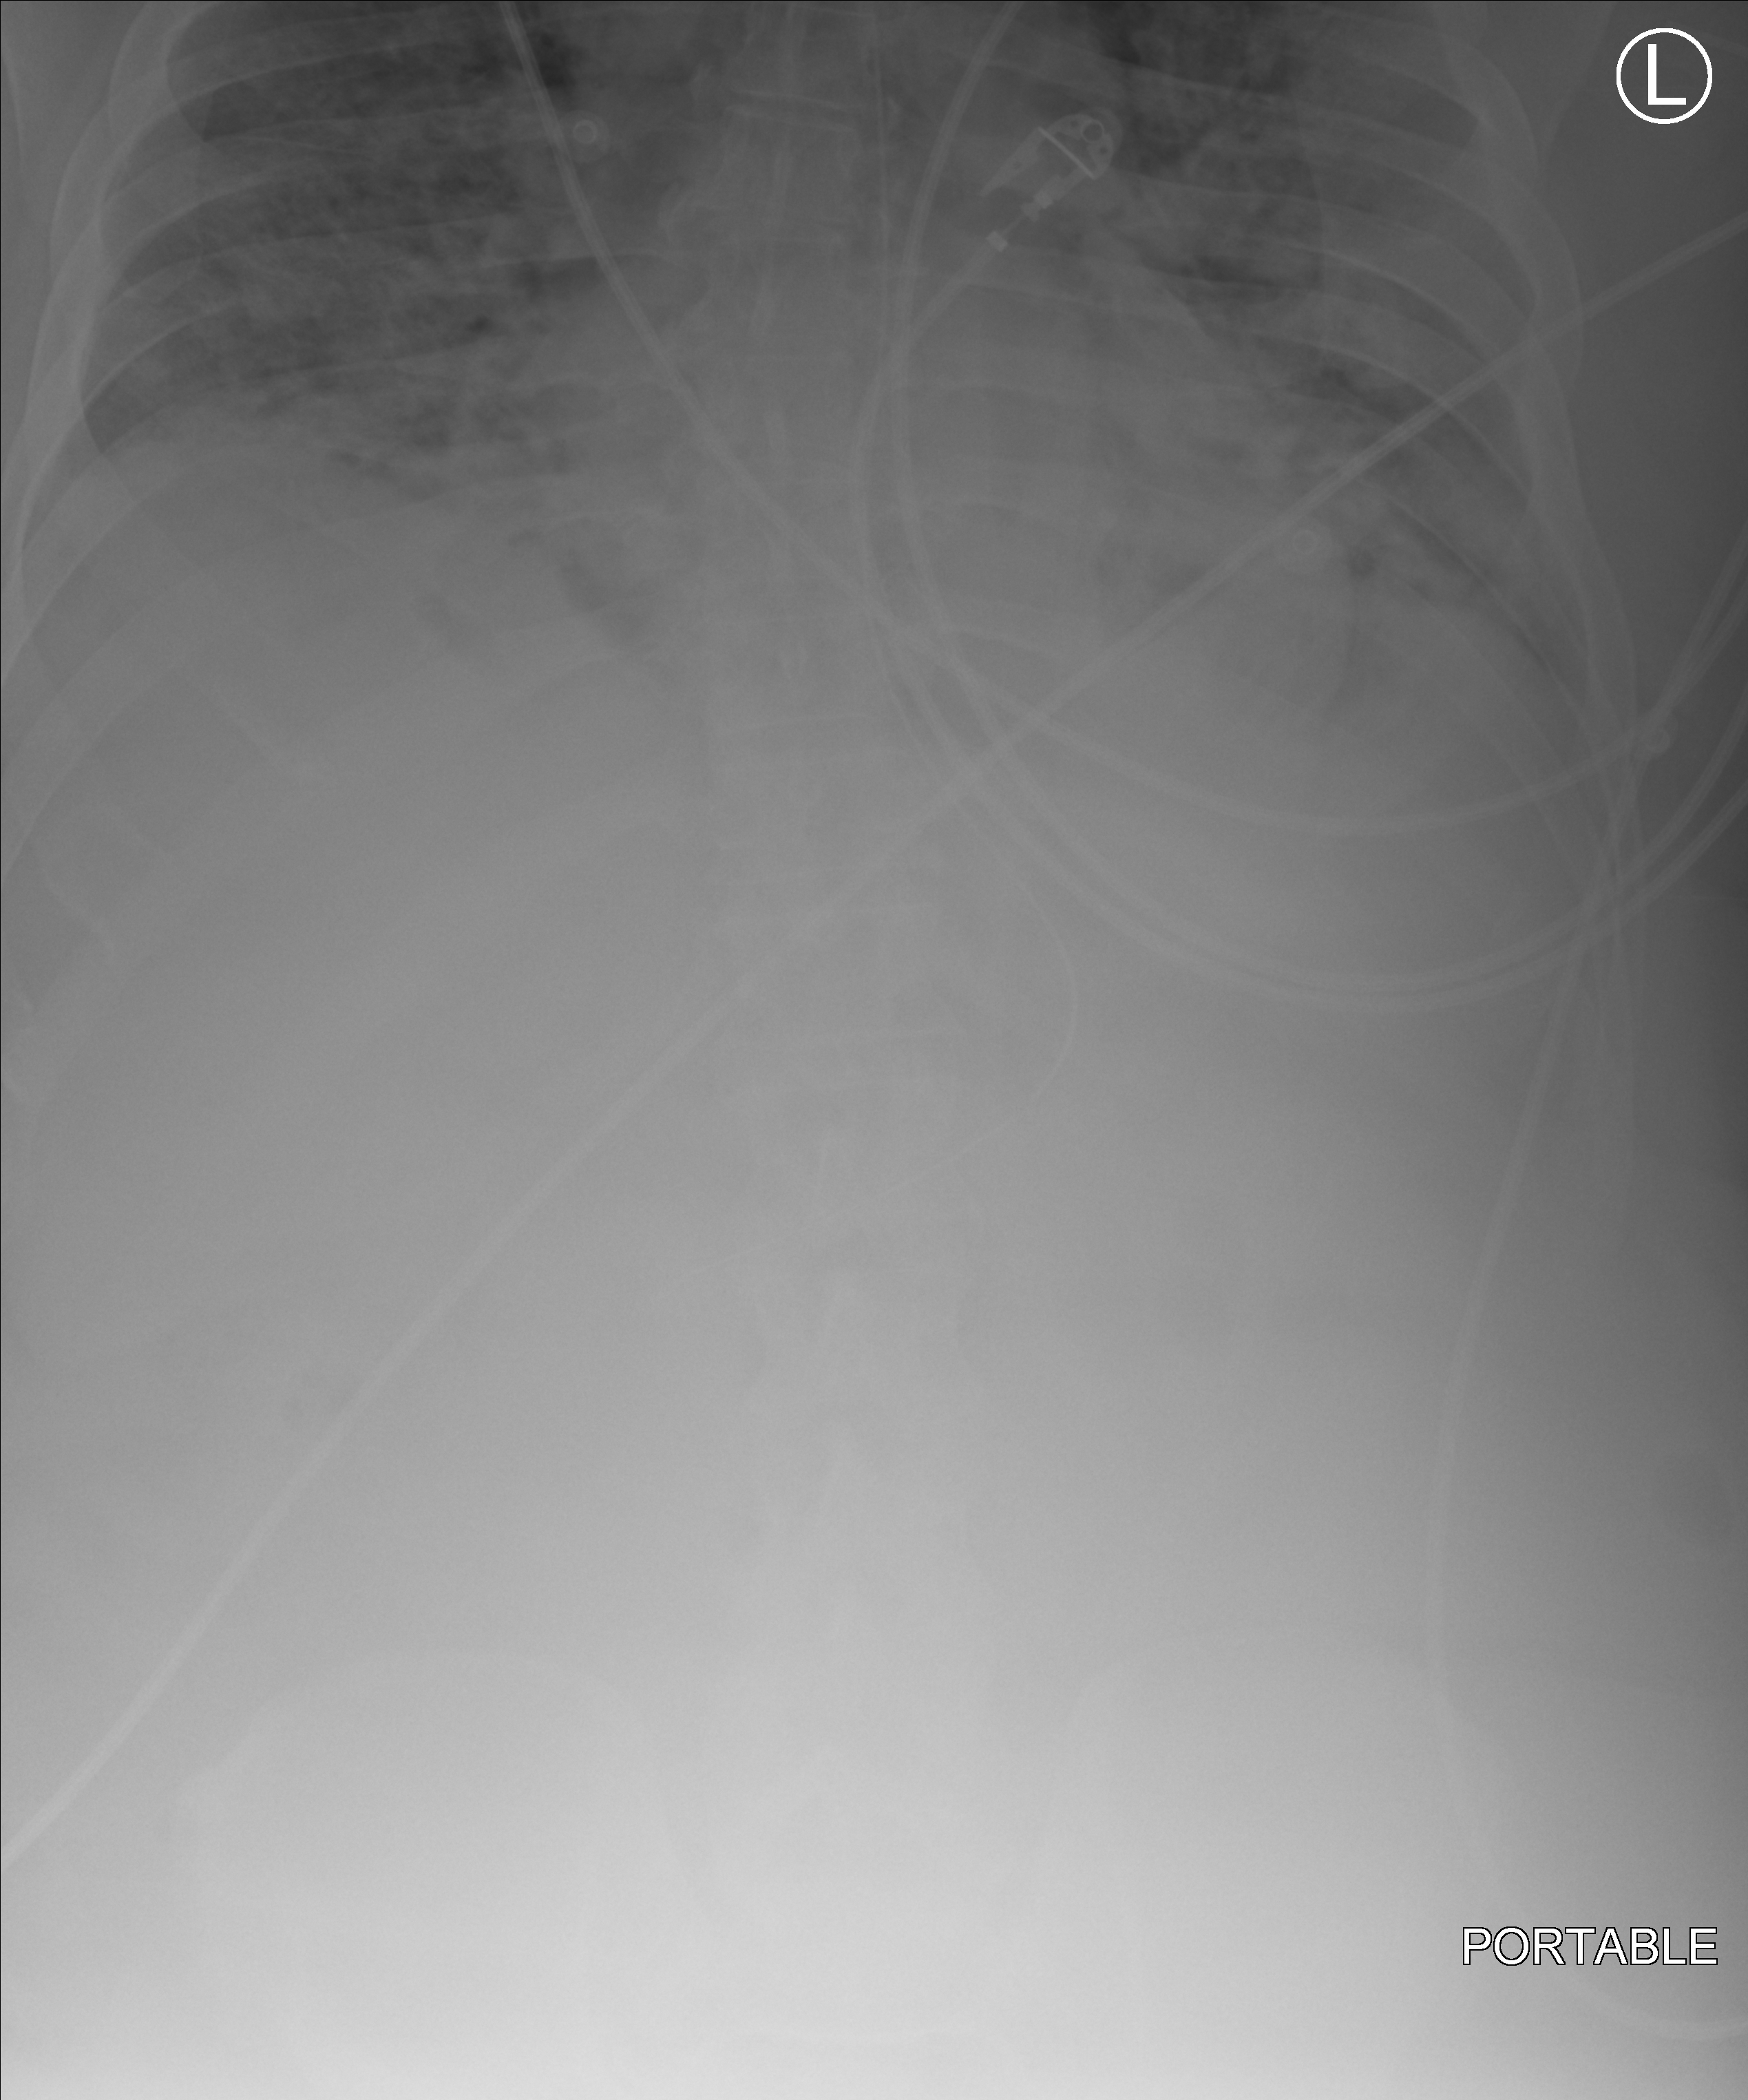
Portable chest radiograph, anteroposterior (AP) projection. Male patient hospitalised with COVID-19, age 18–59 years.
Hospital-stay facts (about this admission, not read from this image; timing relative to this image not recorded):
- admitted to intensive care during this hospital stay: yes
- diabetes (admission record): no